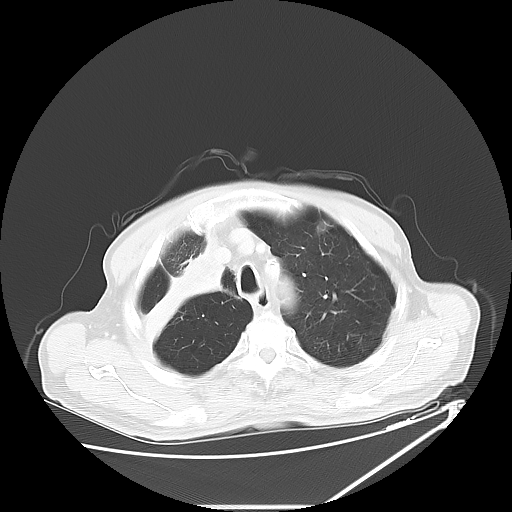
Chest CT, one axial slice; slice 50 of 60 in the series (ordered by position); lung window (W 1500 / L -600 HU); 5 mm slice thickness; 512 × 512 image matrix, field of view 410 × 410 mm. Patient: male, 73 years. From the clinical record (not read from this slice): clinical TNM (as recorded): T2a N1 M0.
Annotated regions visible in this slice (bounding box drawn by a radiologist):
- lung tumour (recorded histology: squamous cell carcinoma): bounding box [x1, y1, x2, y2] px = [137, 239, 241, 349]